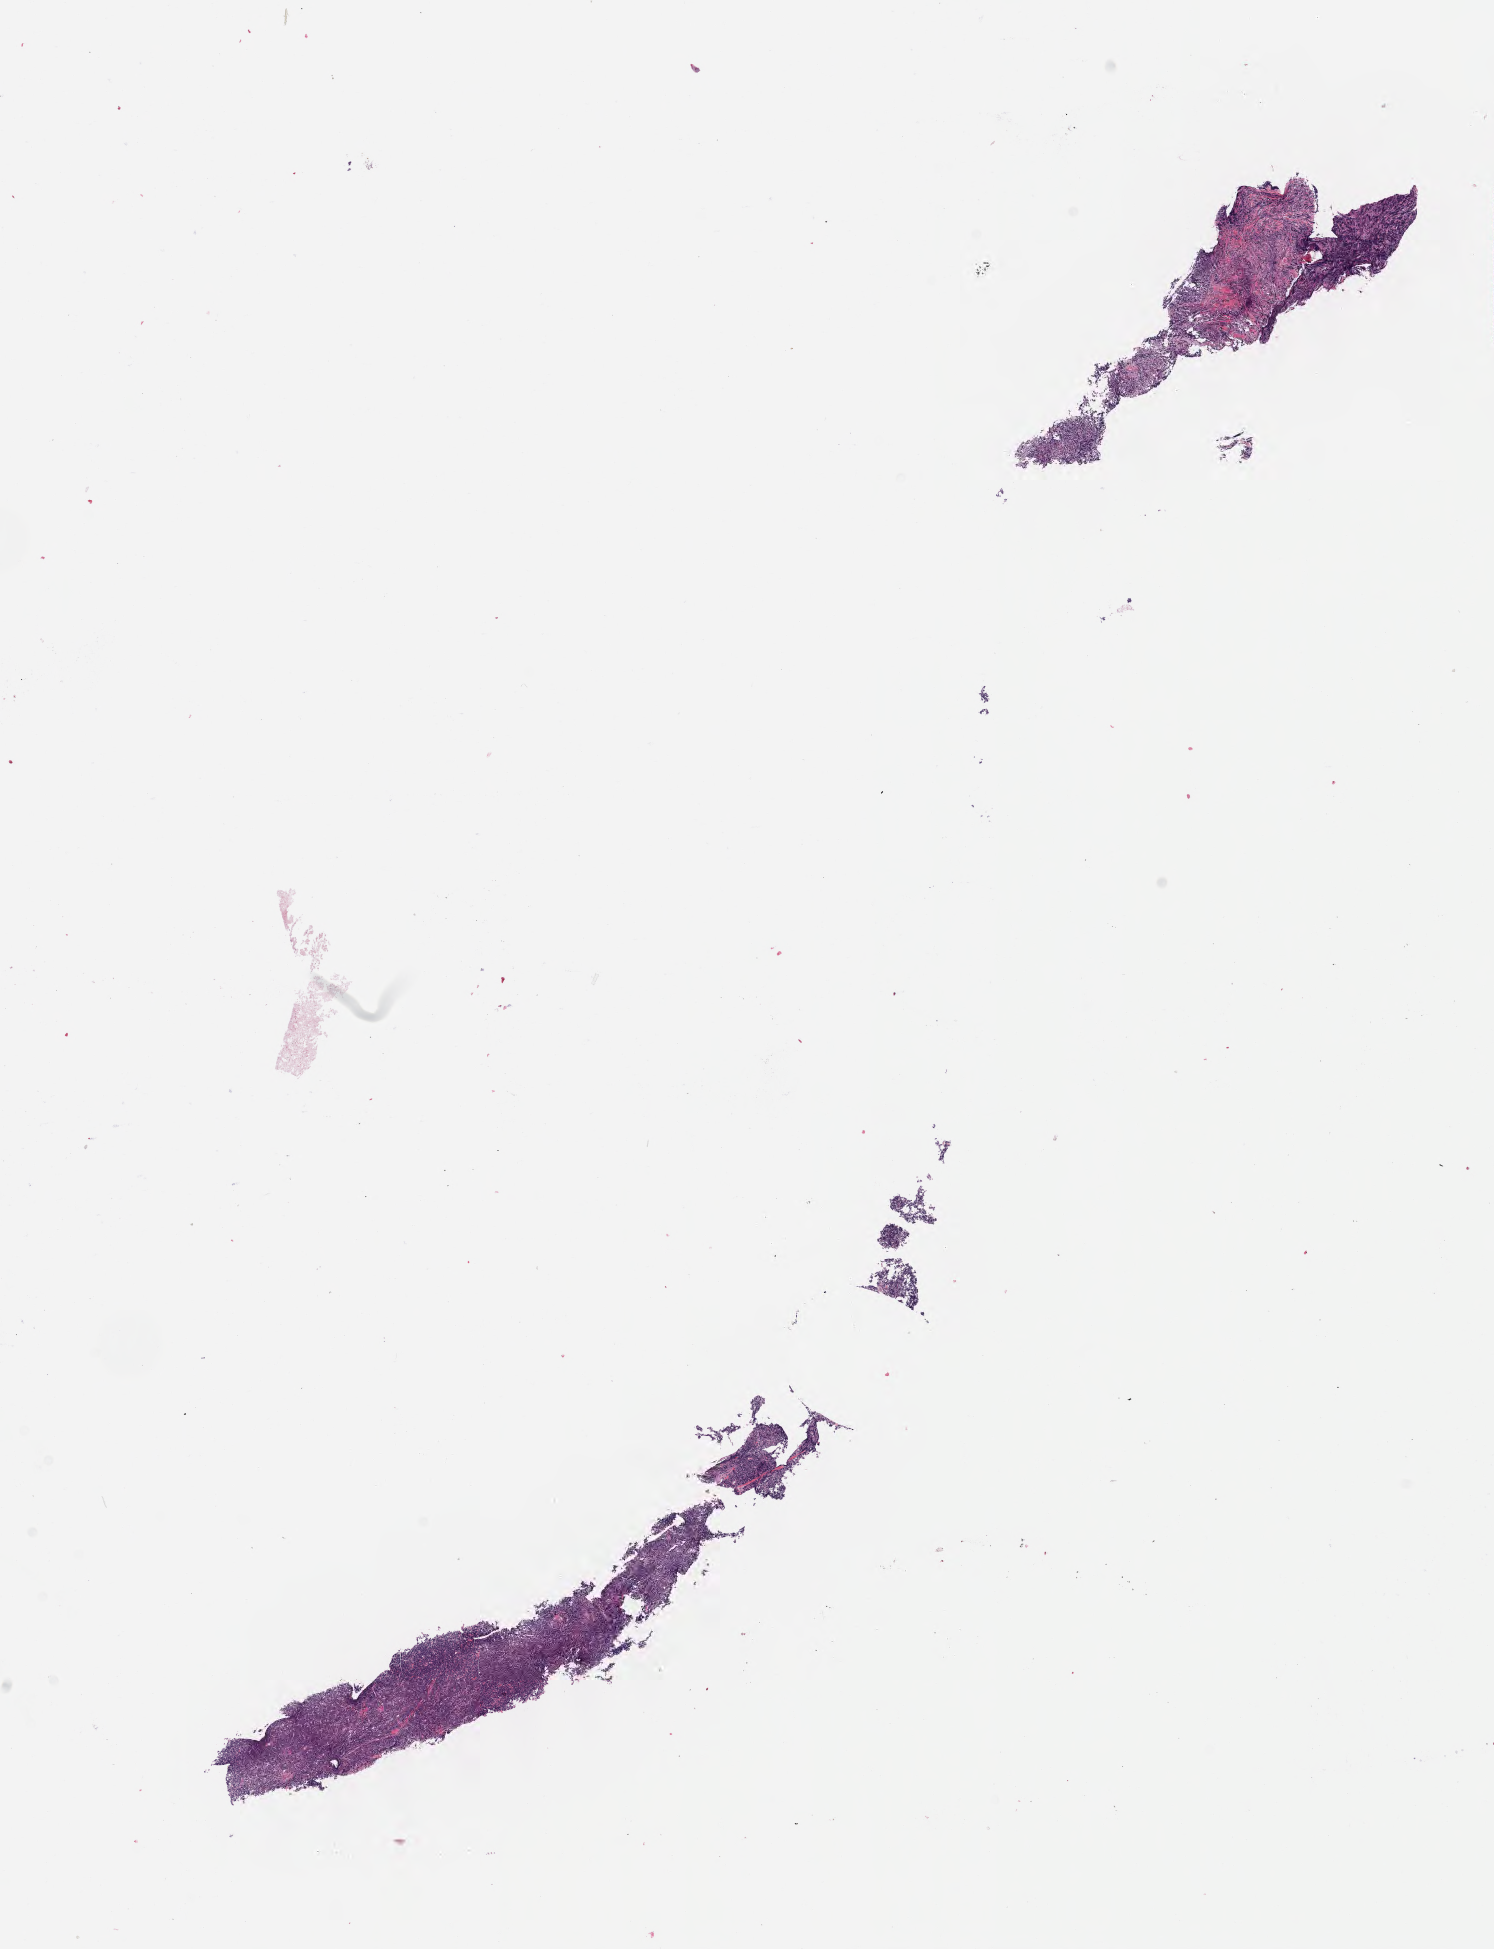
Digitized hematoxylin and eosin (H&E)-stained section, a low-resolution overview of the entire scanned area, about 12.1 x 15.7 mm, tumor tissue, anatomic site: cranium. Female patient; age at initial diagnosis 7 years.
Diagnosis: Burkitt lymphoma, NOS.